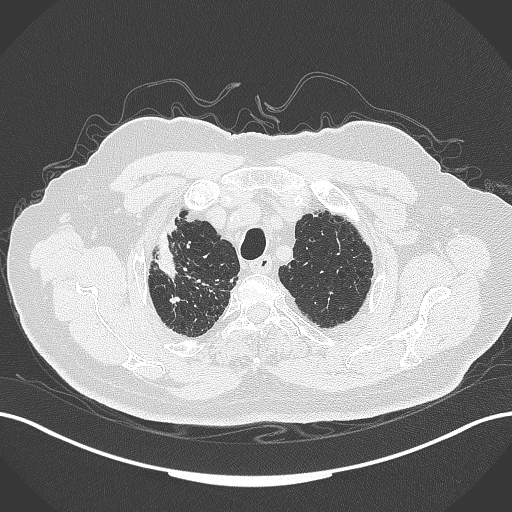
Chest CT, one axial slice; position 307 of 389 along the scan axis; 120 kVp; lung window (W 1500 / L -600 HU); 512 × 512 image matrix, field of view 400 × 400 mm. Patient: male, 72 years. From the clinical record (not read from this slice): clinical TNM (as recorded): T1a N0 M0.
Structures marked on this image (rectangle marked by the reading radiologist):
- lung tumour (recorded histology: squamous cell carcinoma): bounding box <158,225,184,281> (left, top, right, bottom; pixels)